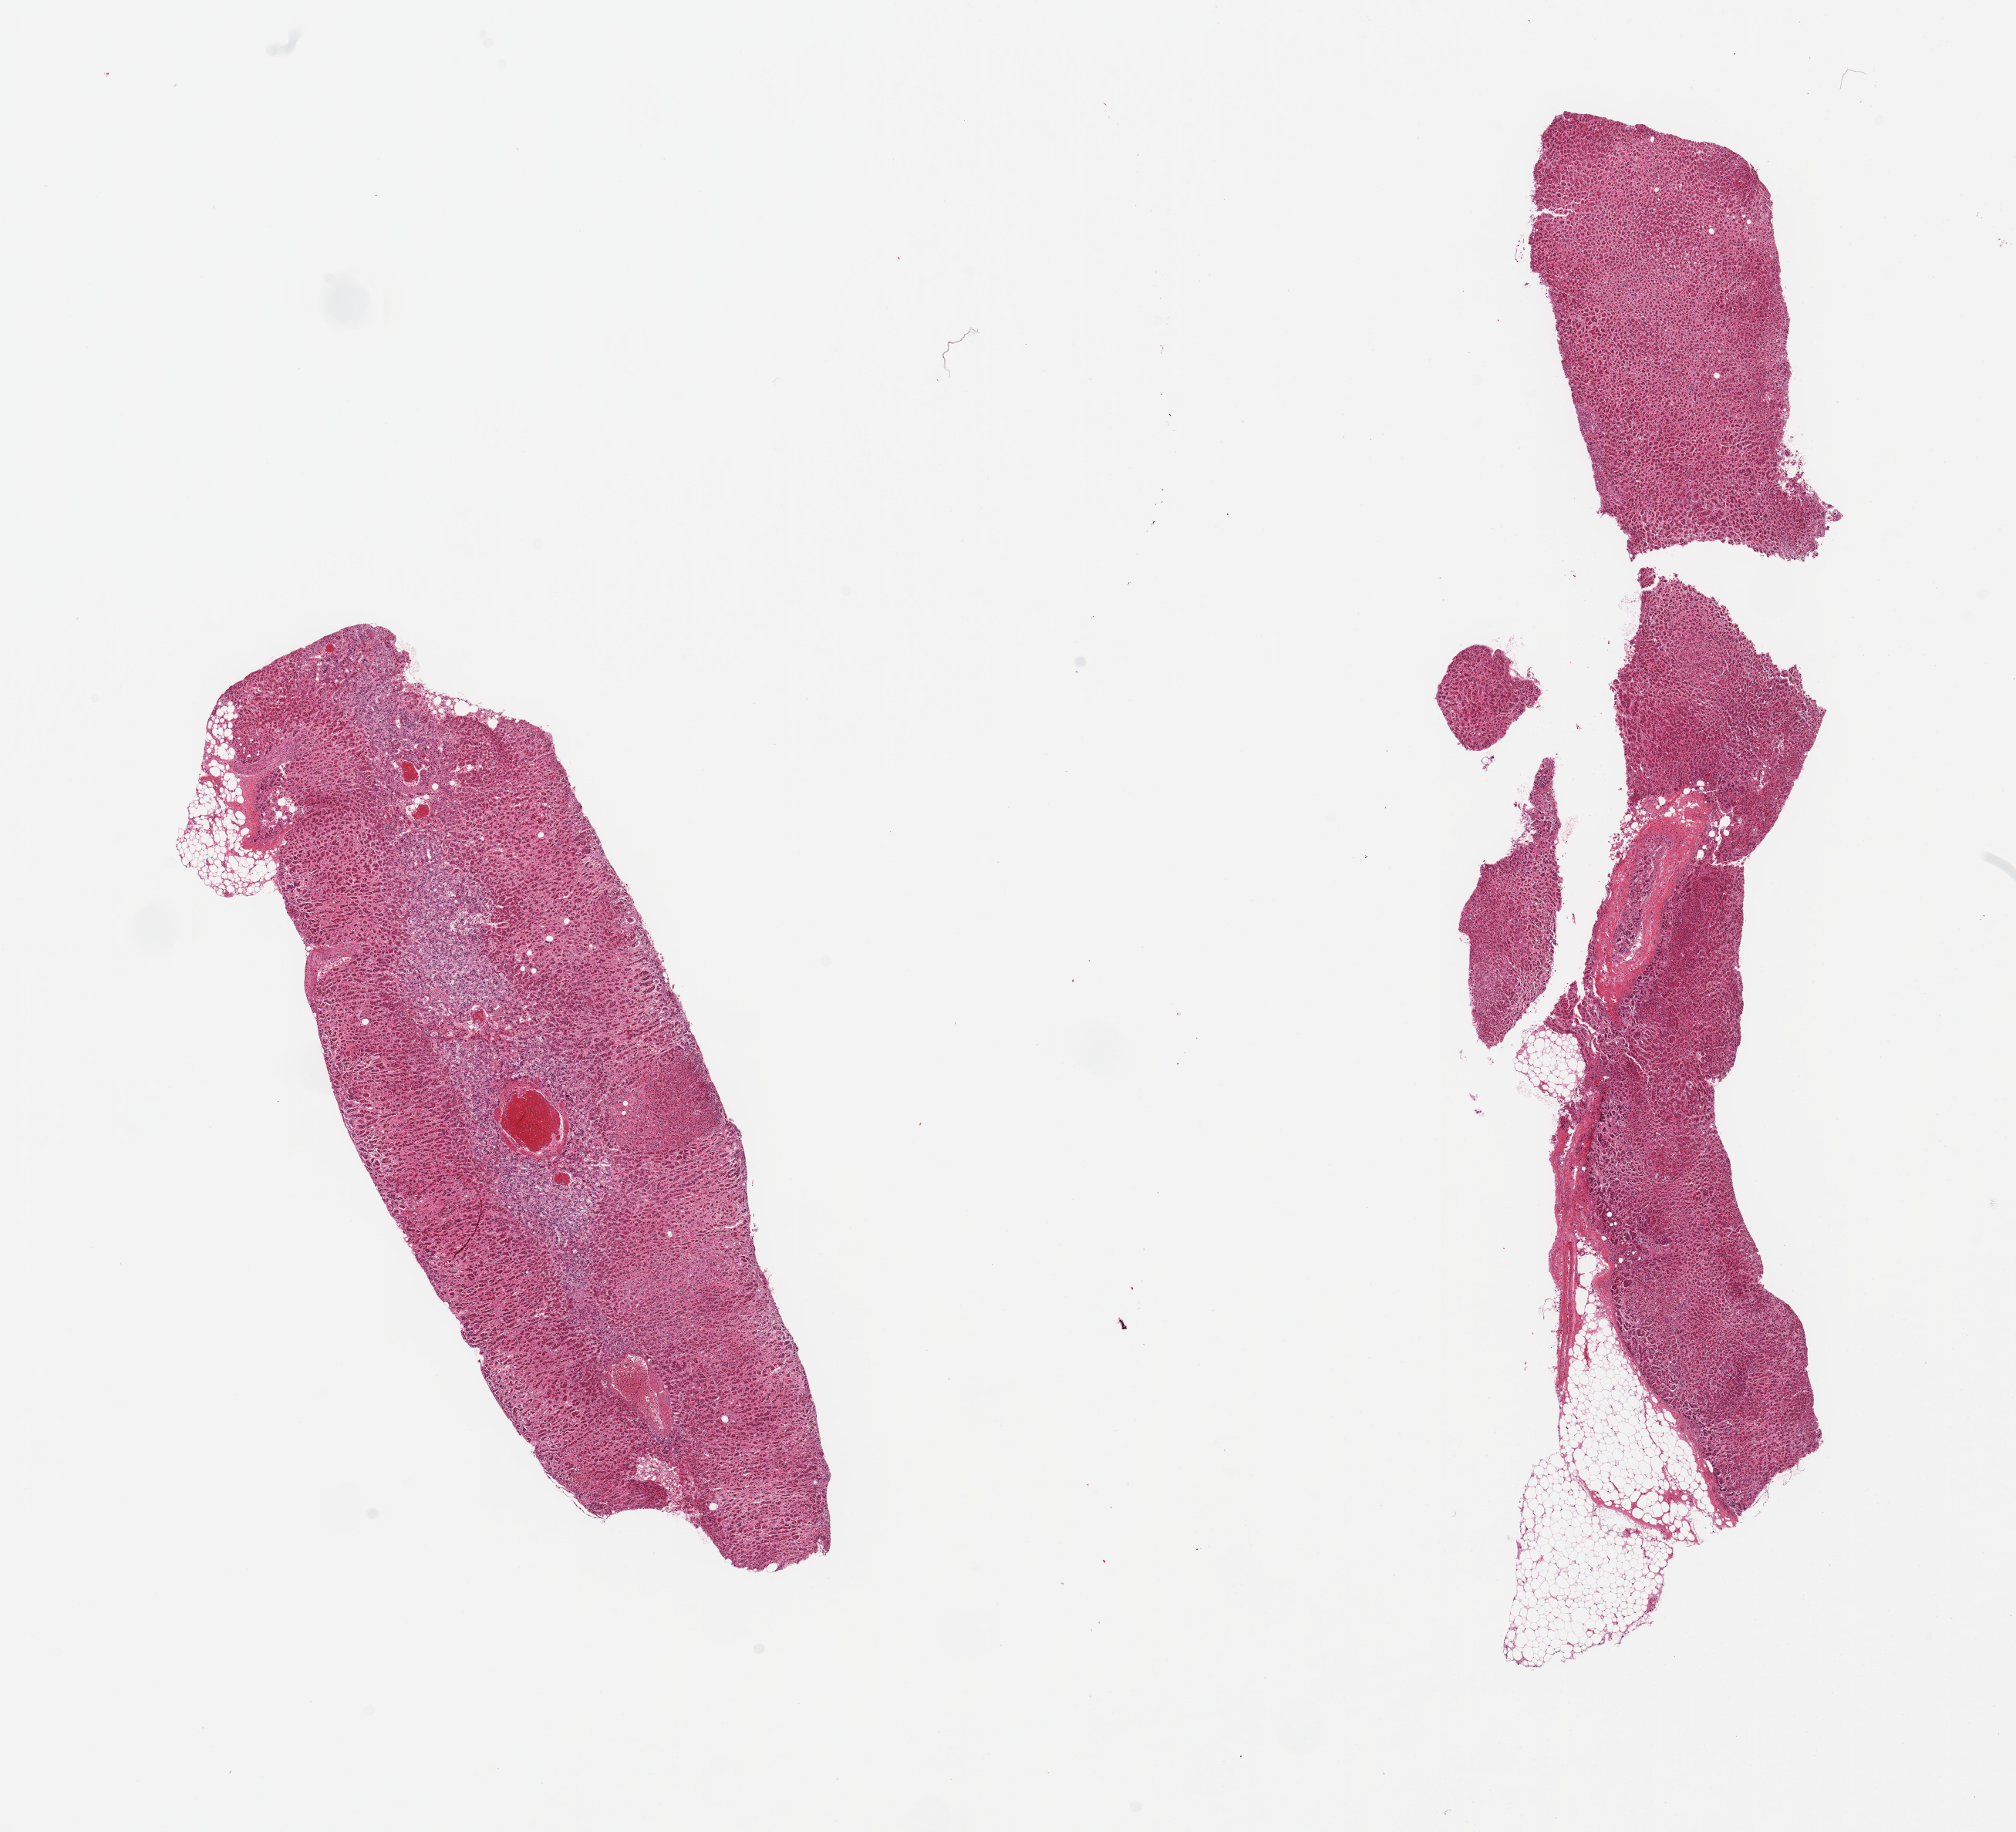
Whole-slide image, haematoxylin and eosin stain — low-resolution overview of the scanned area, about 20.7 x 18.8 mm, PAXgene-fixed, paraffin-embedded tissue, sampled site (target tissue): adrenal gland, donor tissue sample.
* review note (as recorded): 2 pieces; cortex and medulla present; one piece fragmented; 5% and 10% external fat